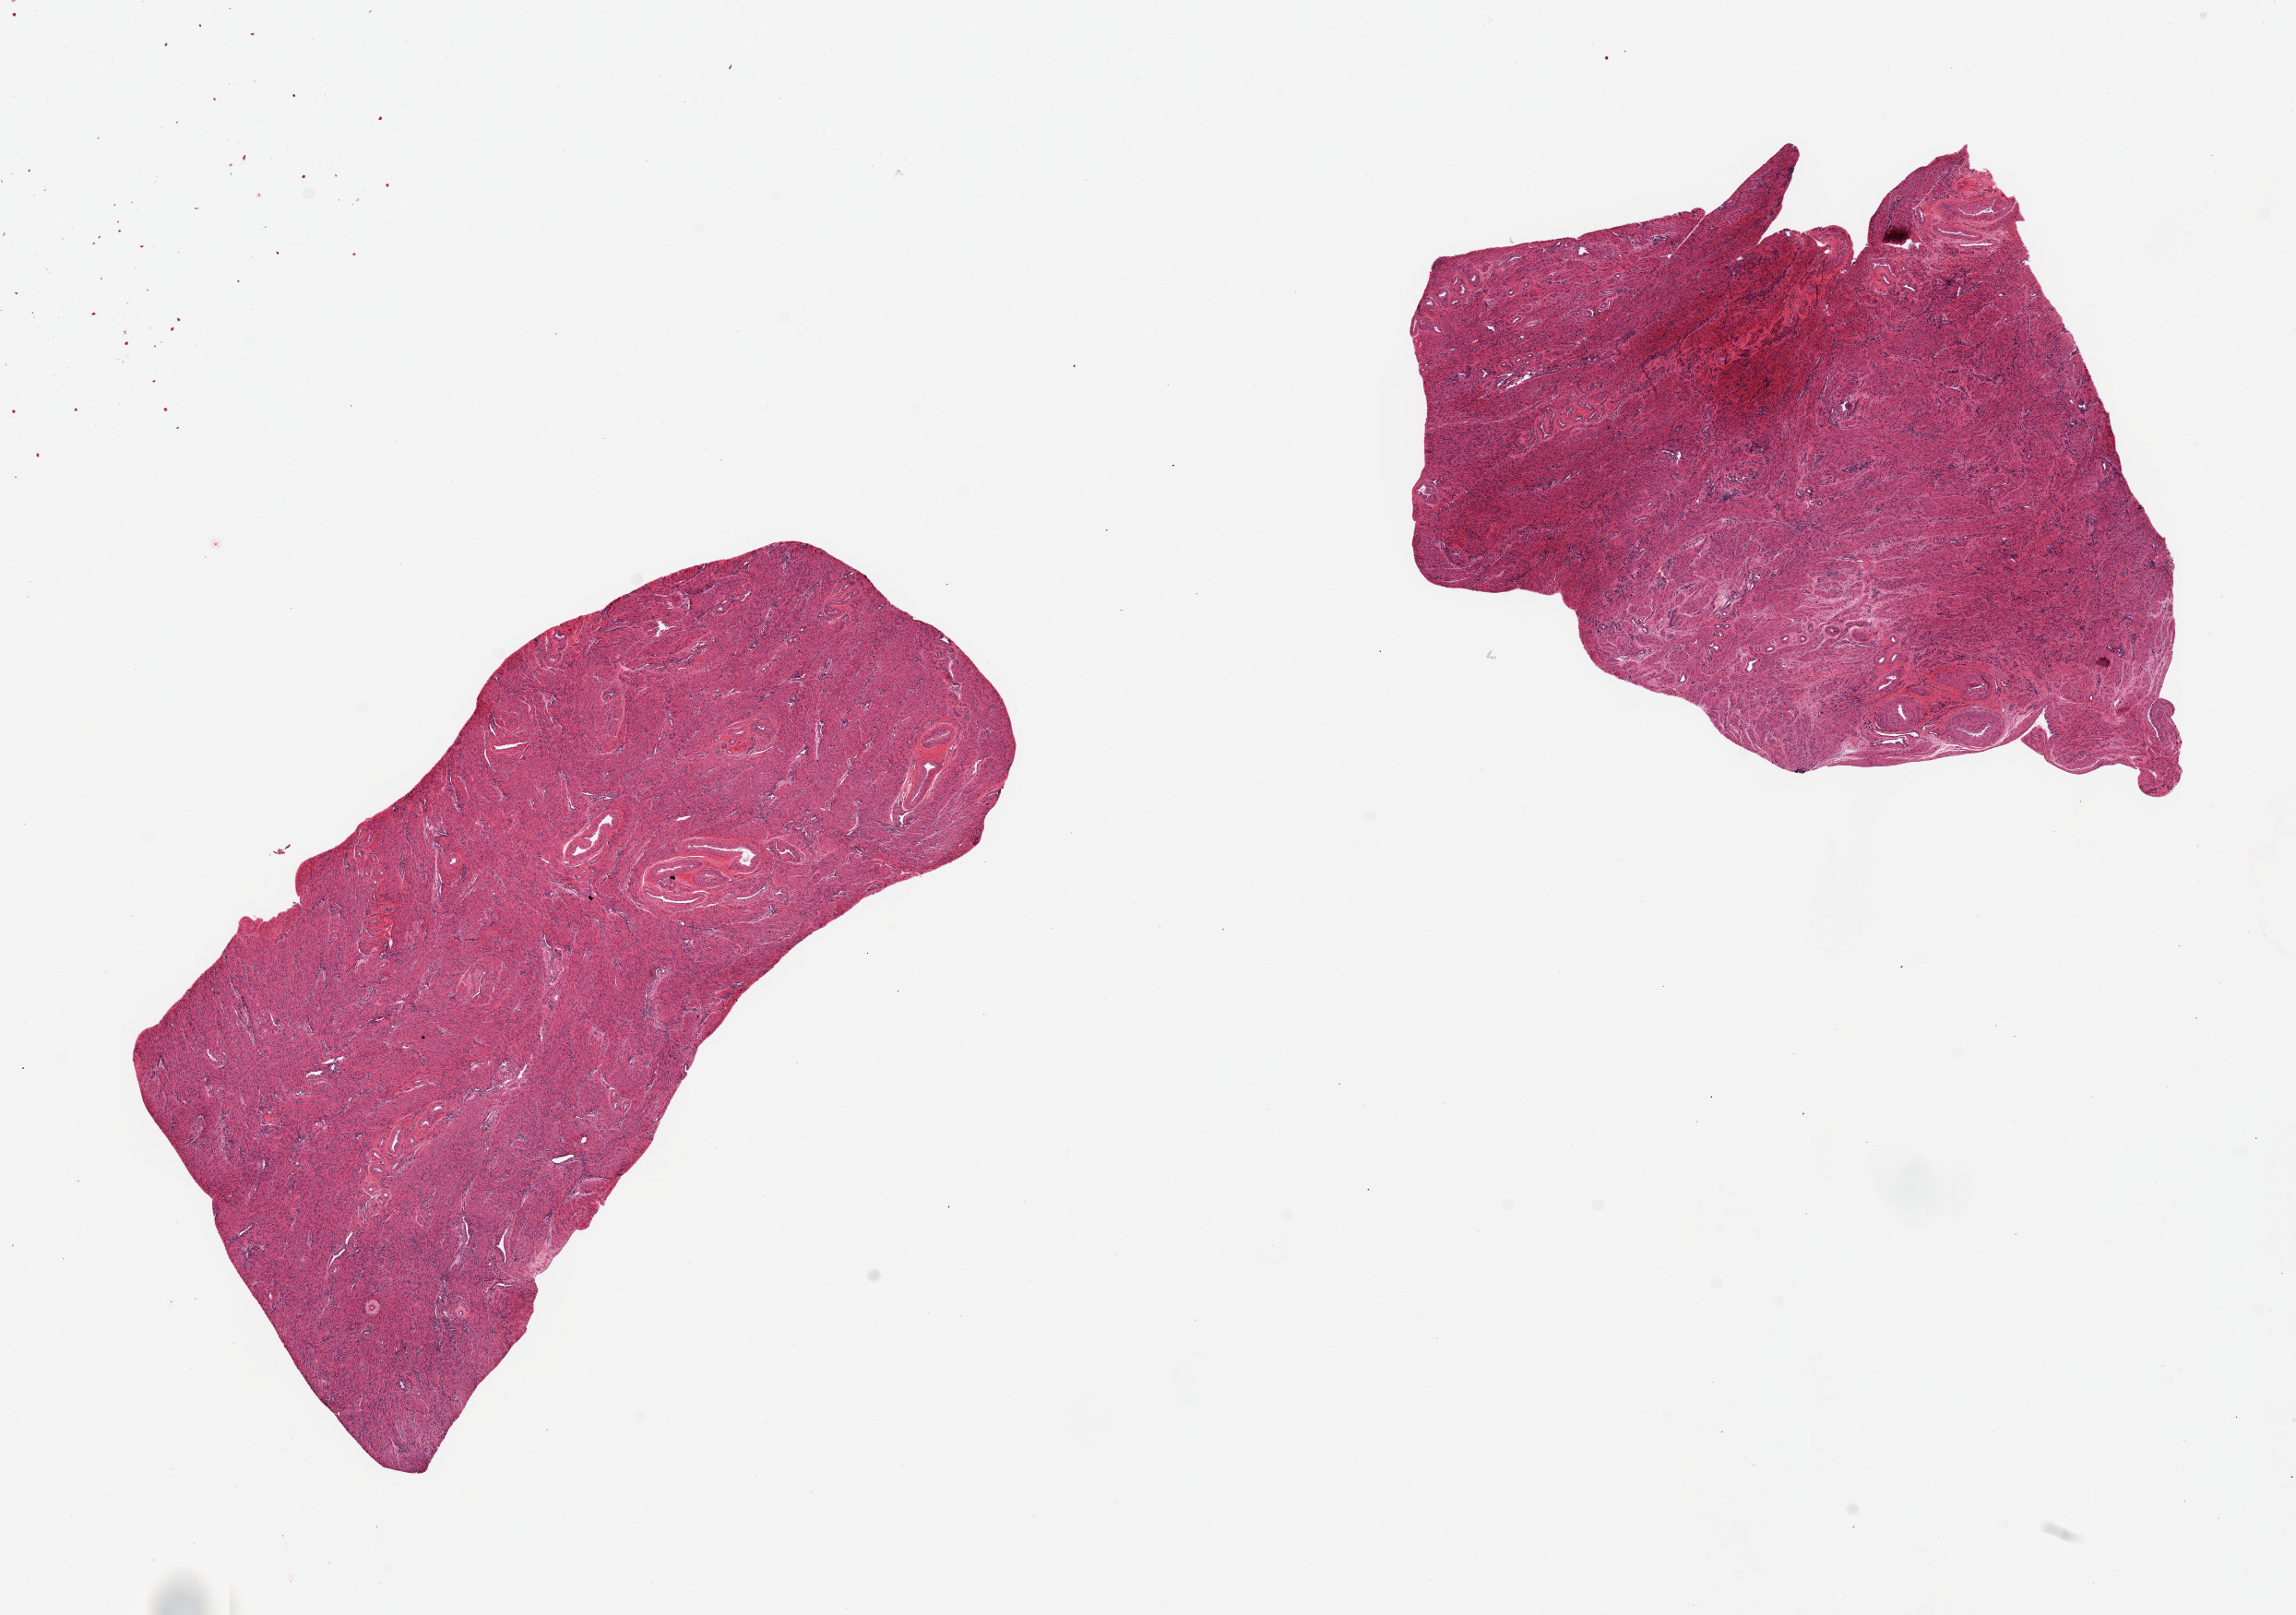
H&E whole-slide image, brightfield, whole scanned area (about 19.7 x 13.9 mm) shown as a low-resolution overview; PAXgene-fixed paraffin-embedded (PFPE) section; target tissue: uterus; tissue donor sample. Donor sex: female.
• pathologist's review note for this sample: 2 pieces